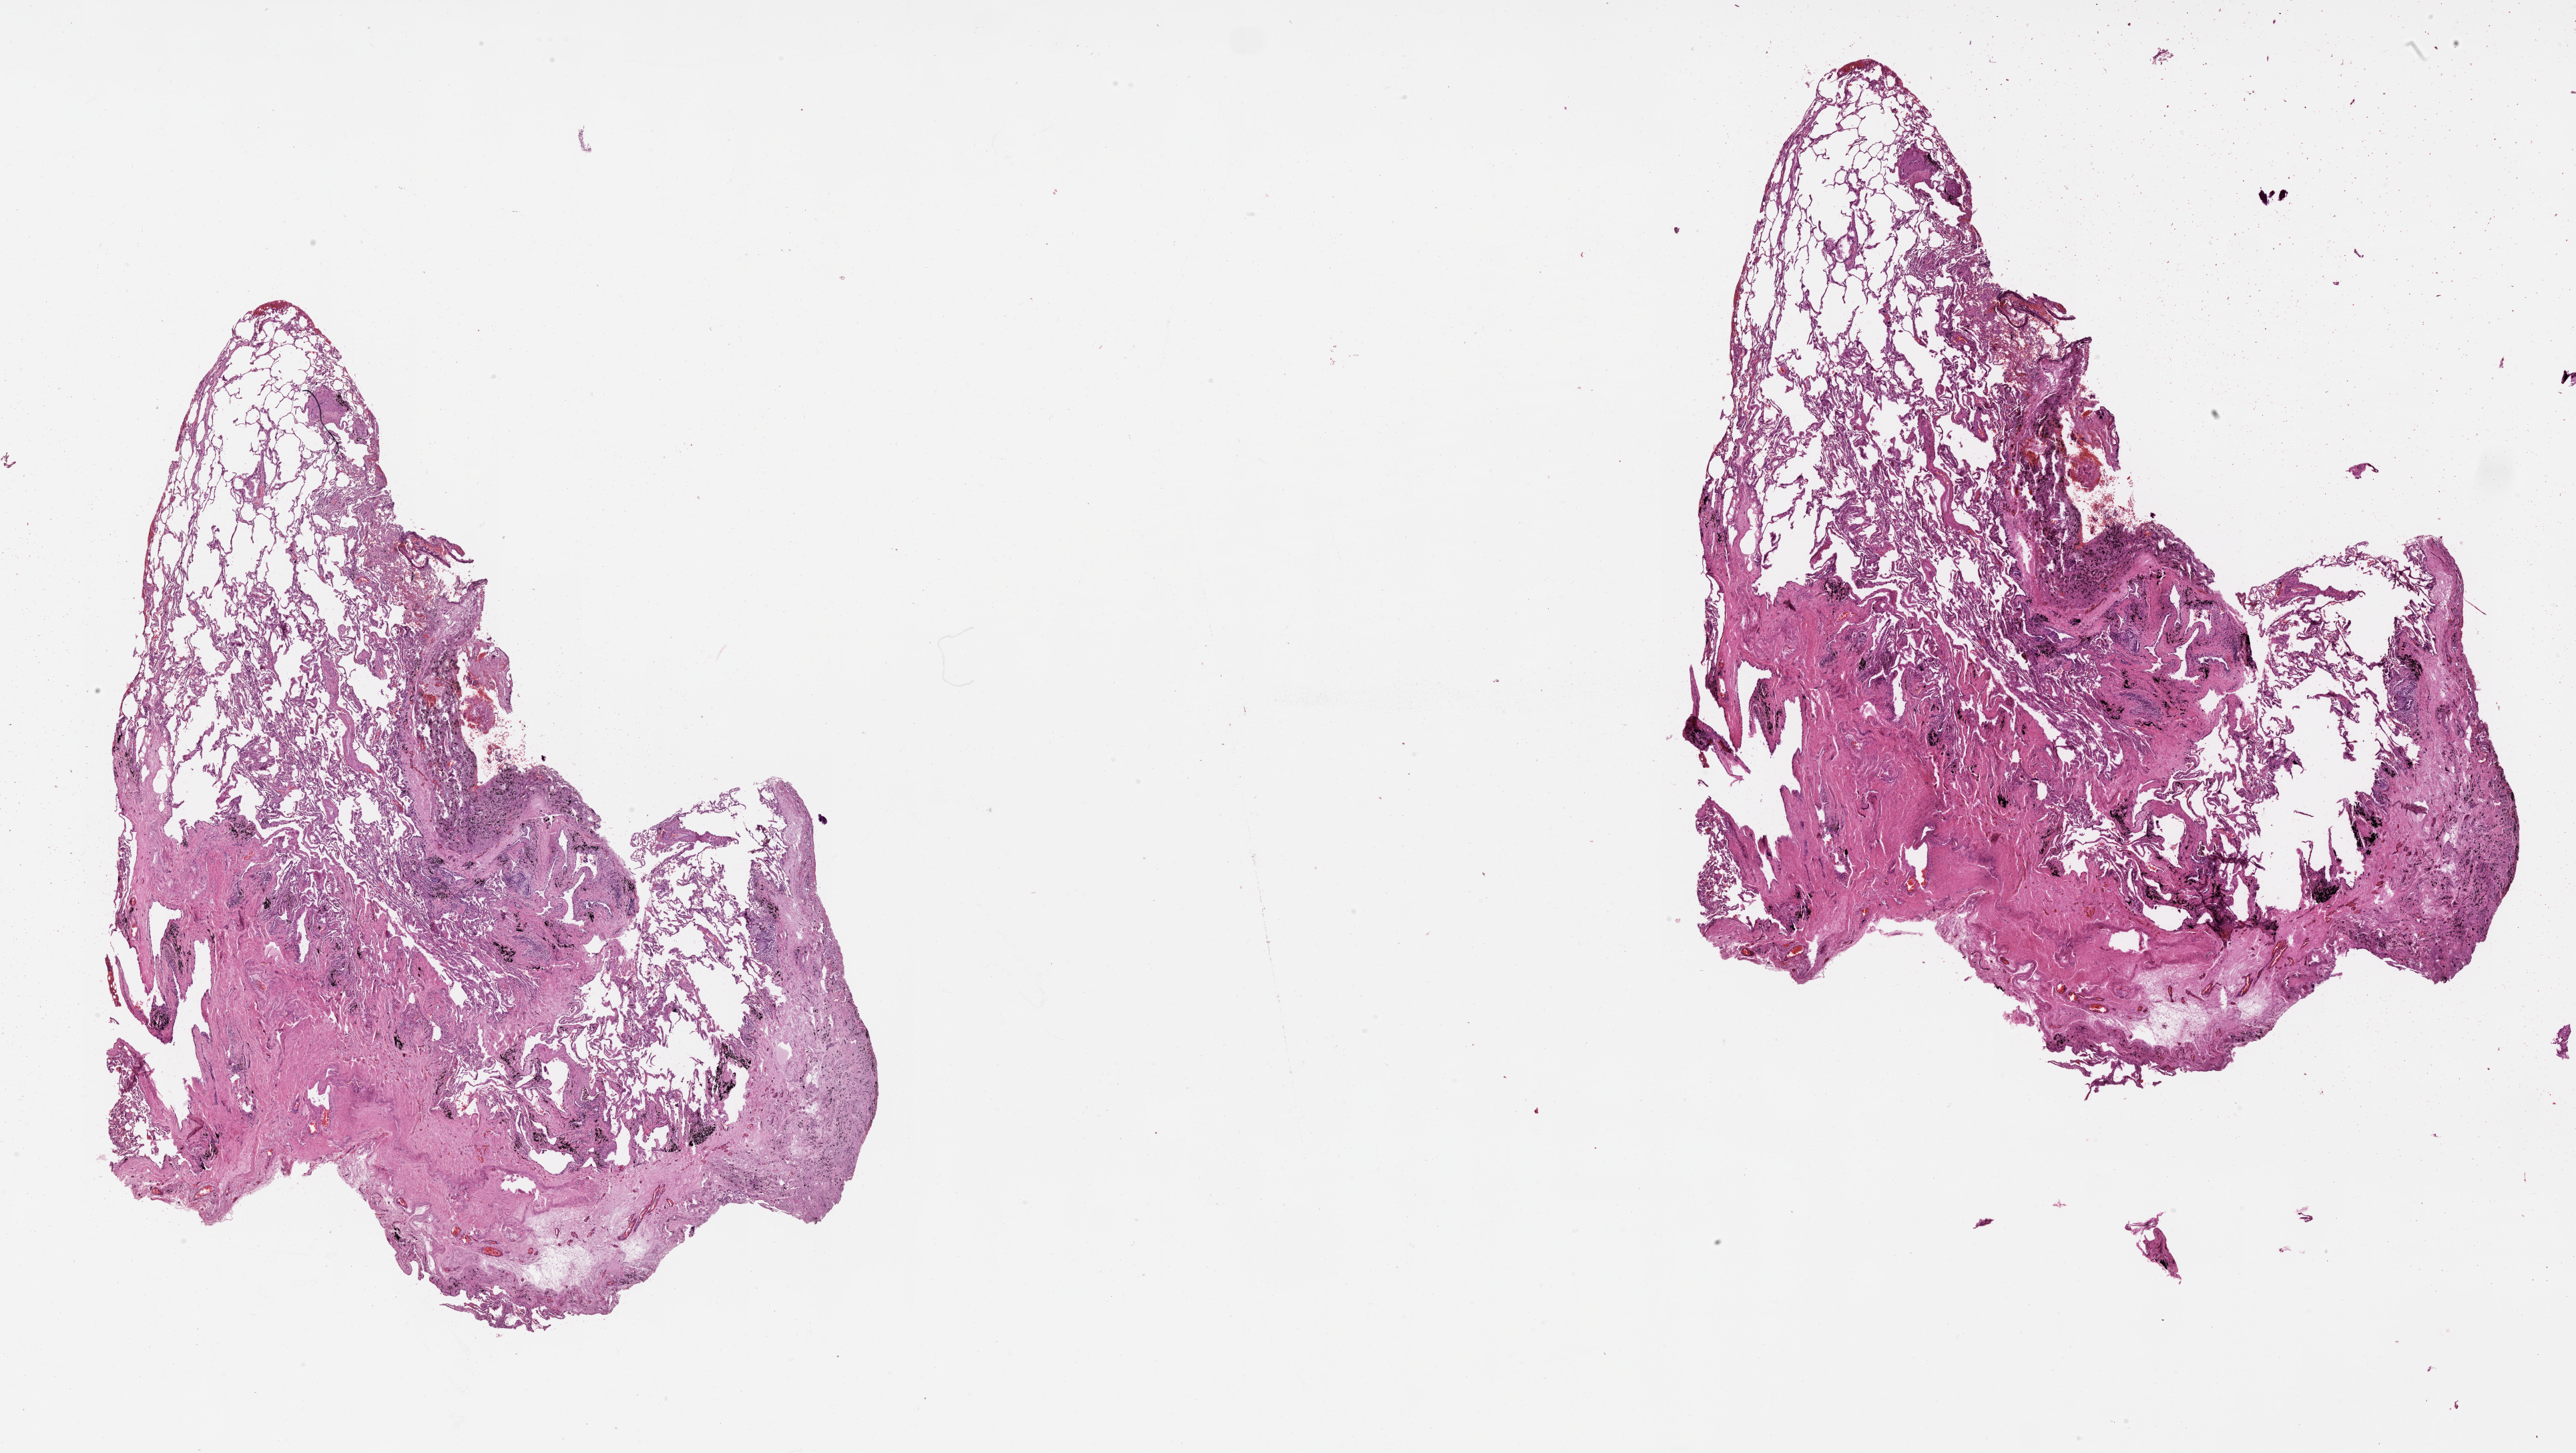
Whole-slide histology image, H&E-stained — low-resolution overview of the scanned area, about 31.1 x 17.5 mm; normal (non-tumour) tissue sample, lung. Patient: male, age 59 years.
This section: normal (non-tumour) tissue from the same patient. Patient diagnosis (cohort enrolment): squamous cell carcinoma (lung).